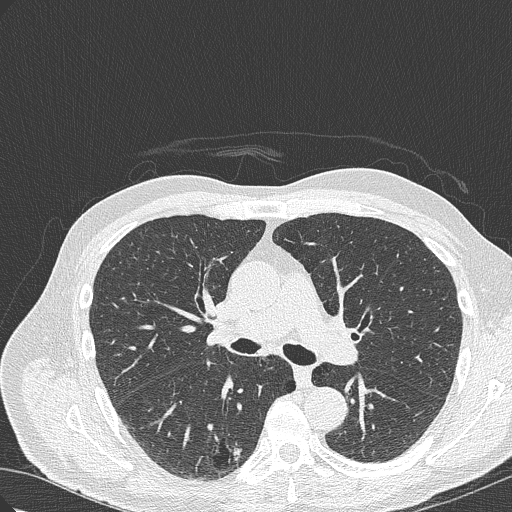
Axial slice from a low-dose chest CT screening exam; first (baseline) screen; lung window (W 1500 / L -600 HU); 120 kVp; 512 × 512 image matrix, field of view 350 × 350 mm. Male participant, aged 70 years at enrolment.
- Expert-annotated lung lesion, bounding box [x1, y1, x2, y2] px = [200, 419, 264, 471].
- The screening reader recorded 4 non-calcified nodules or masses ≥4 mm on this exam; which of them this box marks is not recorded.
- Official screen result: positive, change unspecified: nodule(s) >= 4 mm or enlarging nodule(s), mass(es), or other non-specific abnormalities suspicious for lung cancer.
- Participant outcome: lung cancer diagnosed 978 days after this screen — bronchiolo-alveolar adenocarcinoma, NOS, right lower lobe, poorly differentiated (G3), stage IB (AJCC 6th edition), 30 mm at pathology.